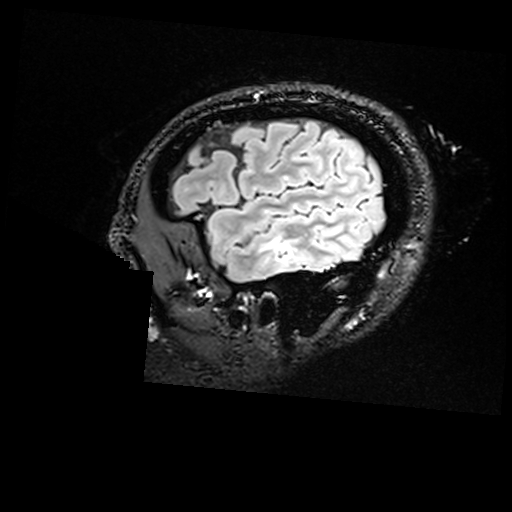
Brain MRI from a brain-tumour surgery series, one sagittal slice; slice 136 of 176 in the series (ordered by position); T2 FLAIR; 1 mm slice thickness; 512 × 512 image matrix. From the clinical record (not read from this slice): histopathology: Non-tumor destructive chronic inflammatory lesion with abnormal vasculature; tumour location: Right Inferior Temporal.
Annotated regions visible in this slice (outlined manually by an expert reader):
- residual tumour: box from (x=280, y=242) to (x=294, y=260) px